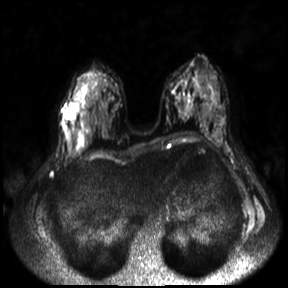
Breast MRI, one axial slice. Position 14 of 30 along the scan axis. Diffusion-weighted series; image 2 of 4 stored at this slice position (different b-values; order by instance number). 3 T. 4 mm slice thickness. 288 × 288 image matrix, field of view 360 × 360 mm. Female patient.
Outlined on this slice (expert manual segmentation):
- tumour on diffusion-weighted imaging: bounding box <65,102,79,118> (left, top, right, bottom; pixels)